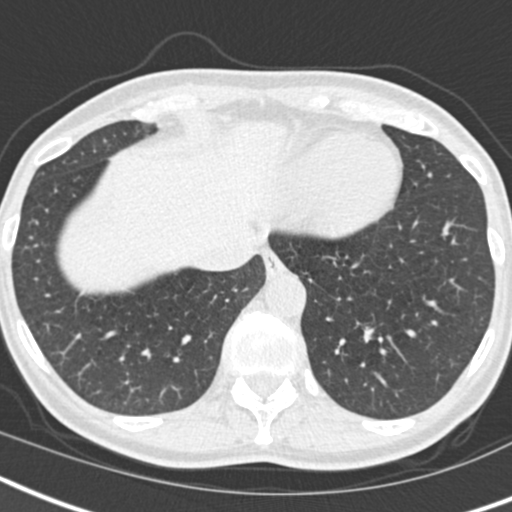
Low-dose screening chest CT, one axial slice; slice 49 of 173 in the series (ordered by position); reconstruction kernel B30f; lung window (W 1500 / L -600 HU); 2 mm slice thickness; 512 × 512 image matrix, field of view 293 × 293 mm.
Annotated regions visible in this slice (expert manual segmentation):
- lesion 1 (tumor, lower lobe of left lung): box from (x=364, y=326) to (x=374, y=342) px